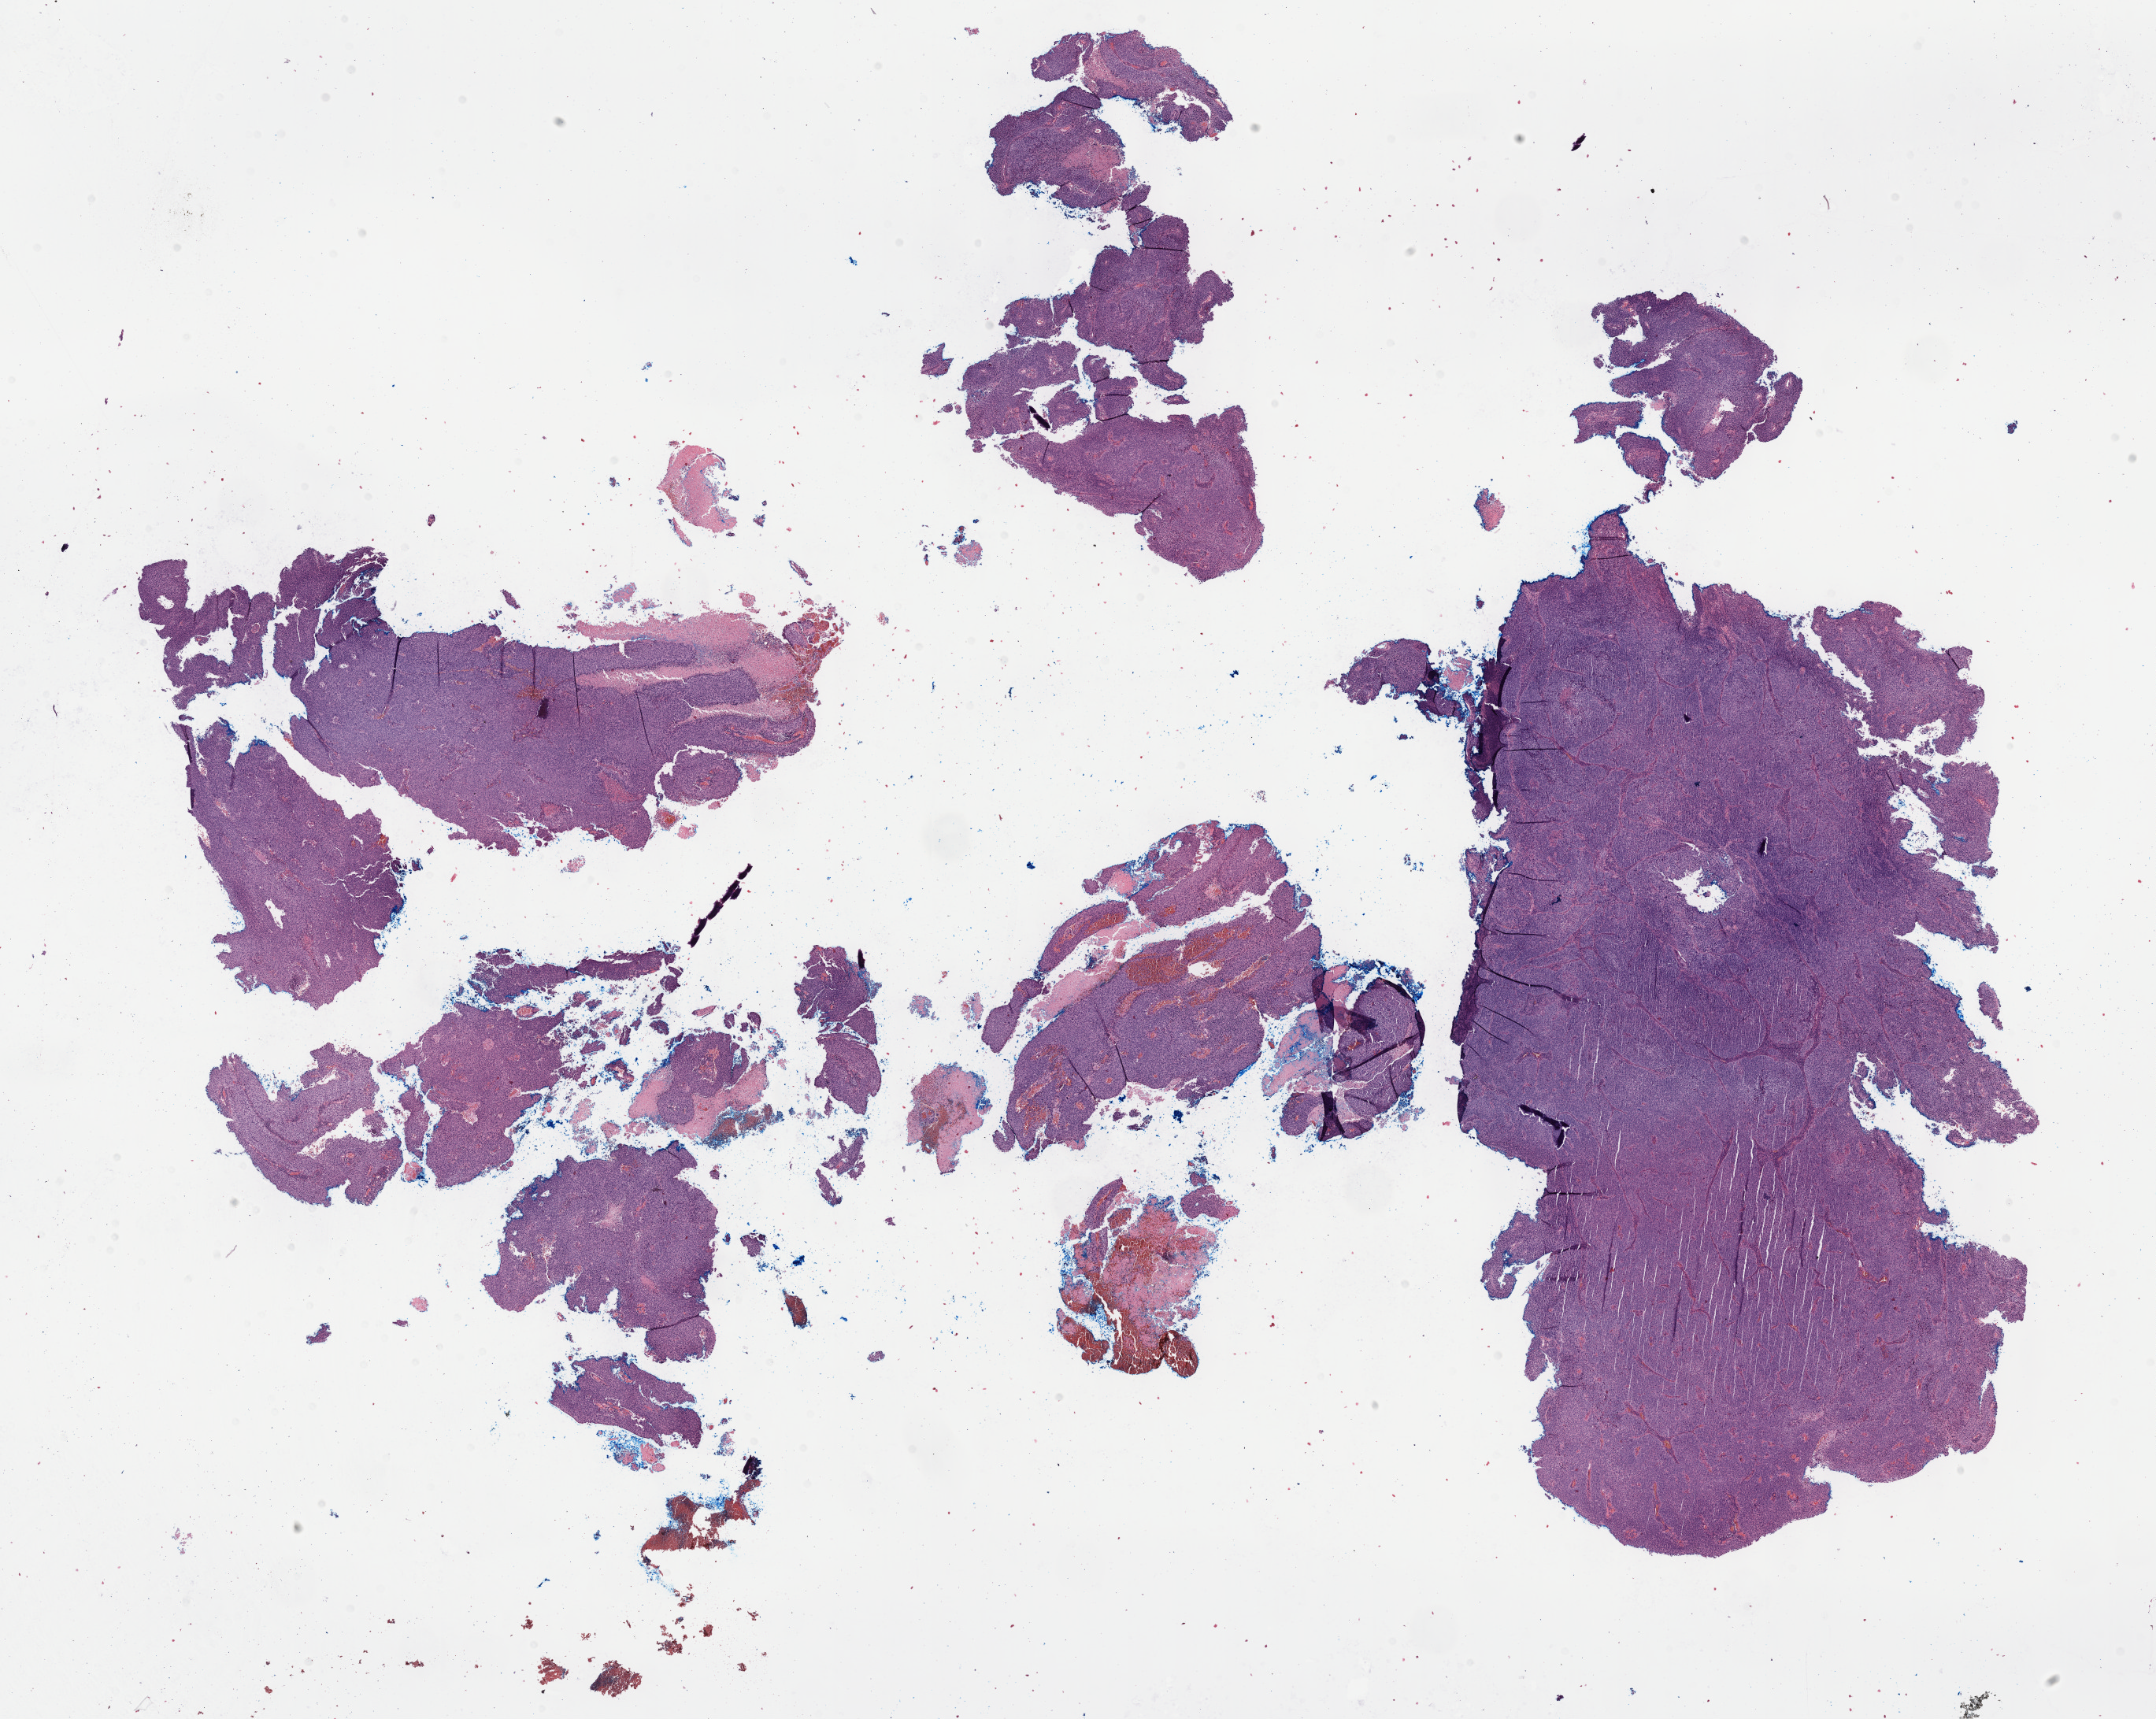
H&E whole-slide image — low-resolution overview of the scanned area, about 22.1 x 17.7 mm, formalin-fixed paraffin-embedded (FFPE) diagnostic section, primary tumour sample from the cervix. Female patient; age at initial diagnosis 73 years. Histologic grade: G2 (moderately differentiated).
• FIGO stage: IIIA
• histologic diagnosis: Squamous cell carcinoma, NOS (cervix uteri)